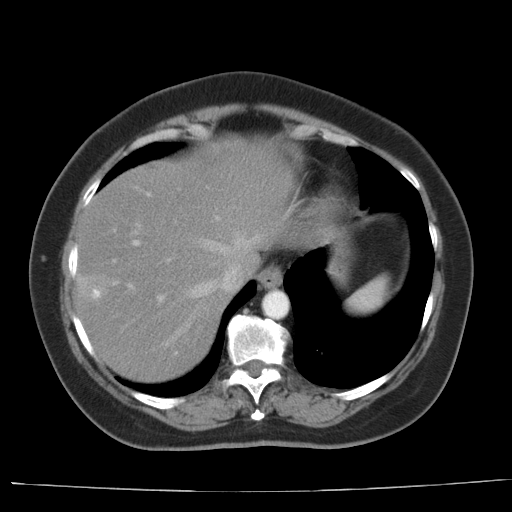
Contrast-enhanced abdominal CT, one axial slice. Position 30 of 44 along the scan axis. Reconstruction kernel AA-1. Soft-tissue window (W 400 / L 40 HU). 5 mm slice thickness. 512 × 512 image matrix, field of view 373 × 373 mm. Female patient. From the clinical record (not read from this slice): diagnosis: colorectal cancer liver metastases, imaged before liver resection.
Outlined on this slice (expert manual segmentation):
- hepatic veins: bounding box <157,232,256,347> (left, top, right, bottom; pixels)
- liver: <76,137,299,385>
- planned liver remnant (the part of the liver to remain after resection): <105,137,299,278>
- portal vein (with intrahepatic branches): <113,193,259,354>